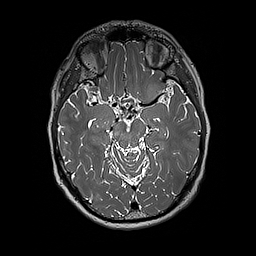
Brain MRI from a brain-tumour surgery series, one axial slice. Slice 117 of 192 in the series (ordered by position). 1 mm slice thickness. 256 × 256 image matrix, field of view 250 × 250 mm. From the clinical record (not read from this slice): histopathology: Glioblastoma; WHO grade: 4; IDH mutation: no; tumour location: Left Insular.
Structures marked on this image (outlined manually by an expert reader):
- tumour: box from (x=140, y=82) to (x=171, y=107) px